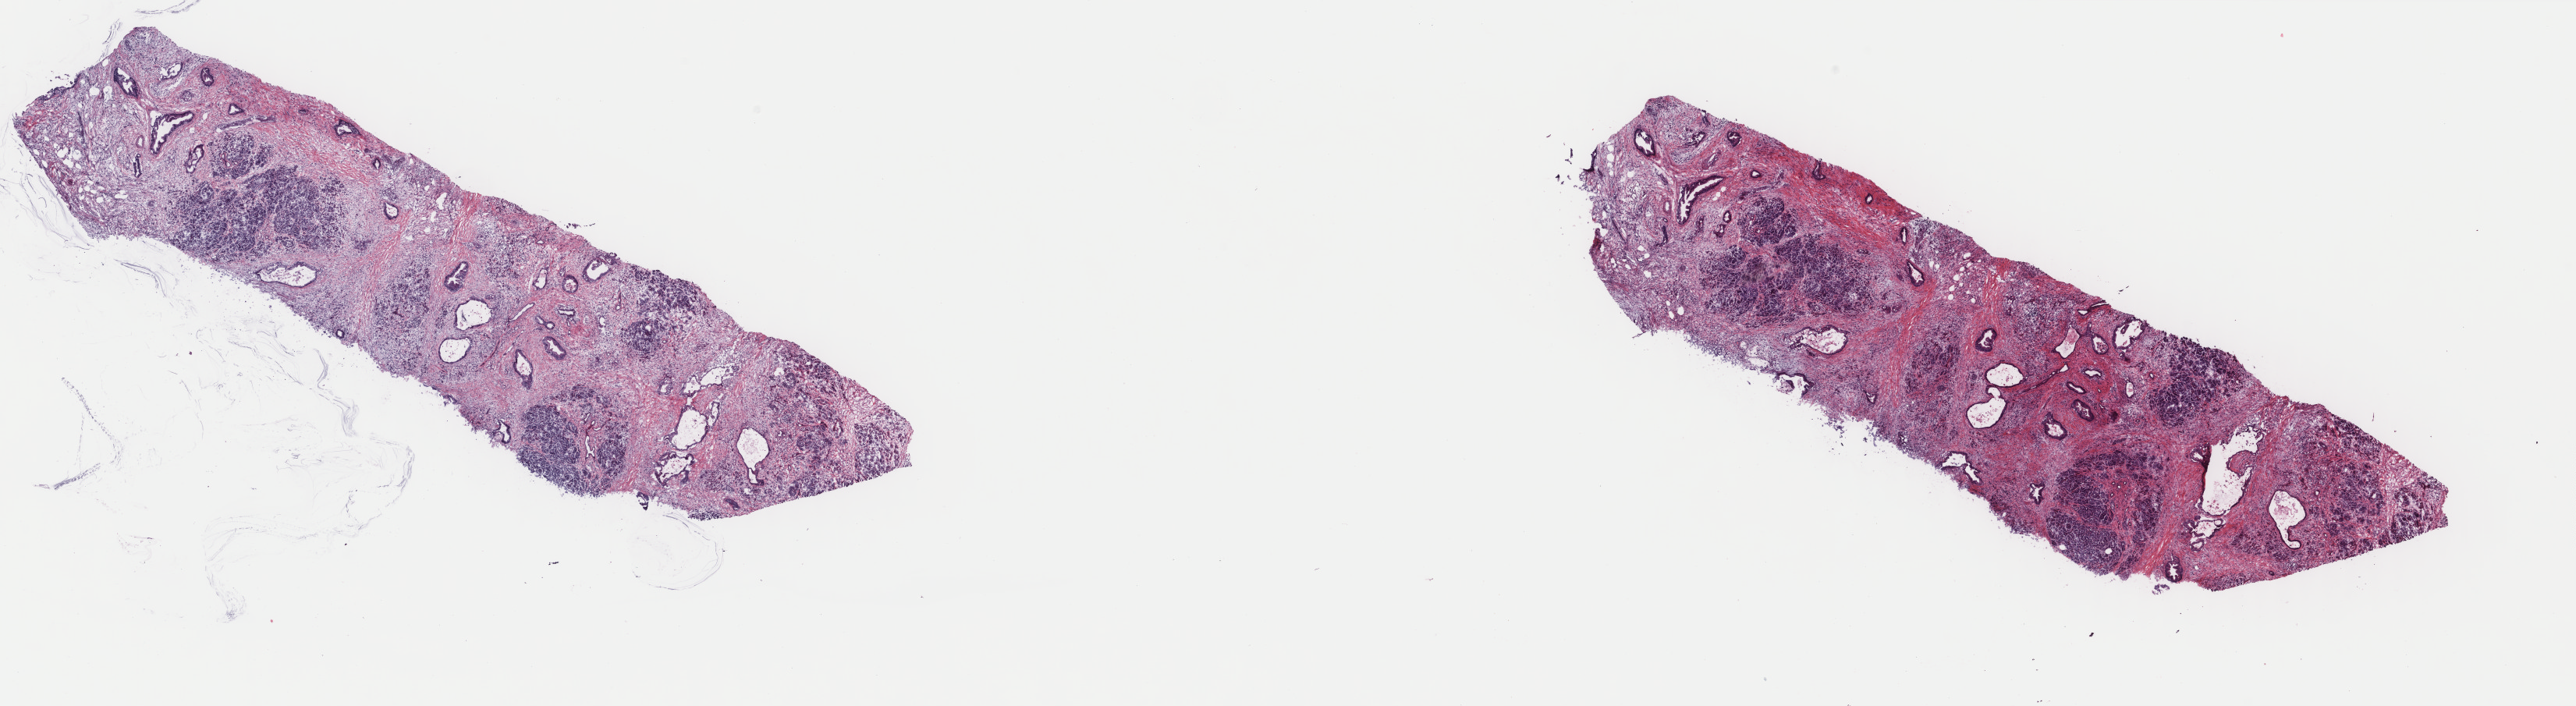
Digitized H&E tissue section (whole slide) — a low-resolution overview of the entire scanned area, about 26.2 x 7.2 mm (from a 40x scan); frozen section; pancreas, primary tumour sample. Patient: female, age at initial diagnosis 71 years. Pathologist review of this section (percent, as recorded): tumour cells 60%, tumour nuclei 10%.
Histologic diagnosis: Infiltrating duct carcinoma, NOS (head of pancreas).